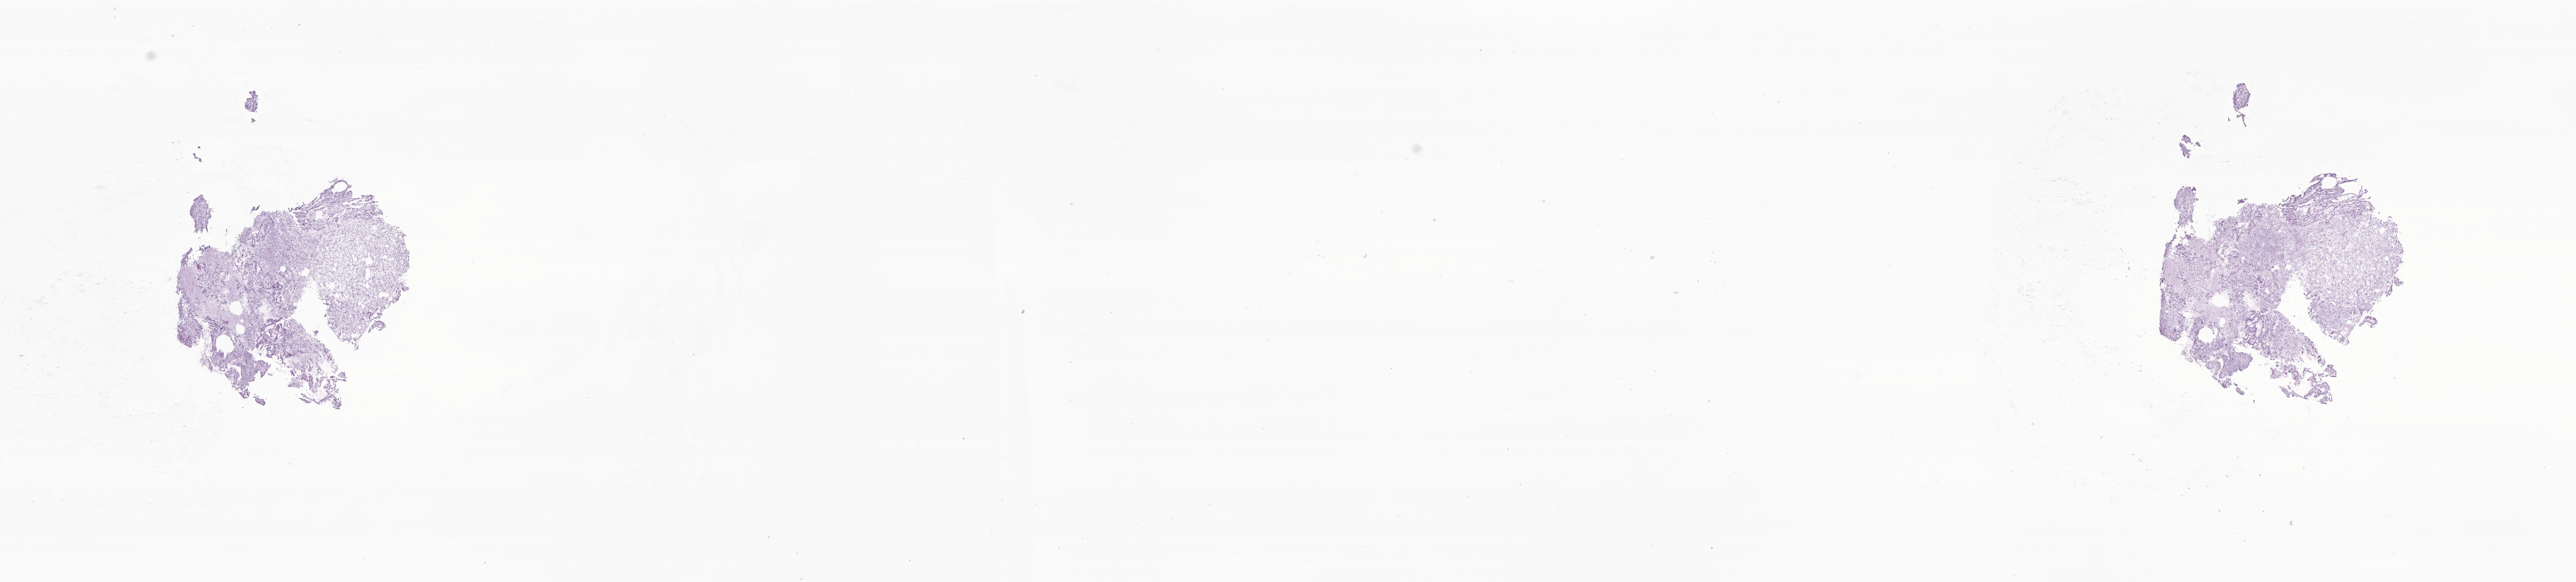
Digitized haematoxylin and eosin-stained section of tumor tissue from the brain — low-resolution overview of the scanned area, about 27.7 x 6.3 mm. Frozen section. Female patient, age 758 days.
Diagnosis: Neoplasm, malignant.